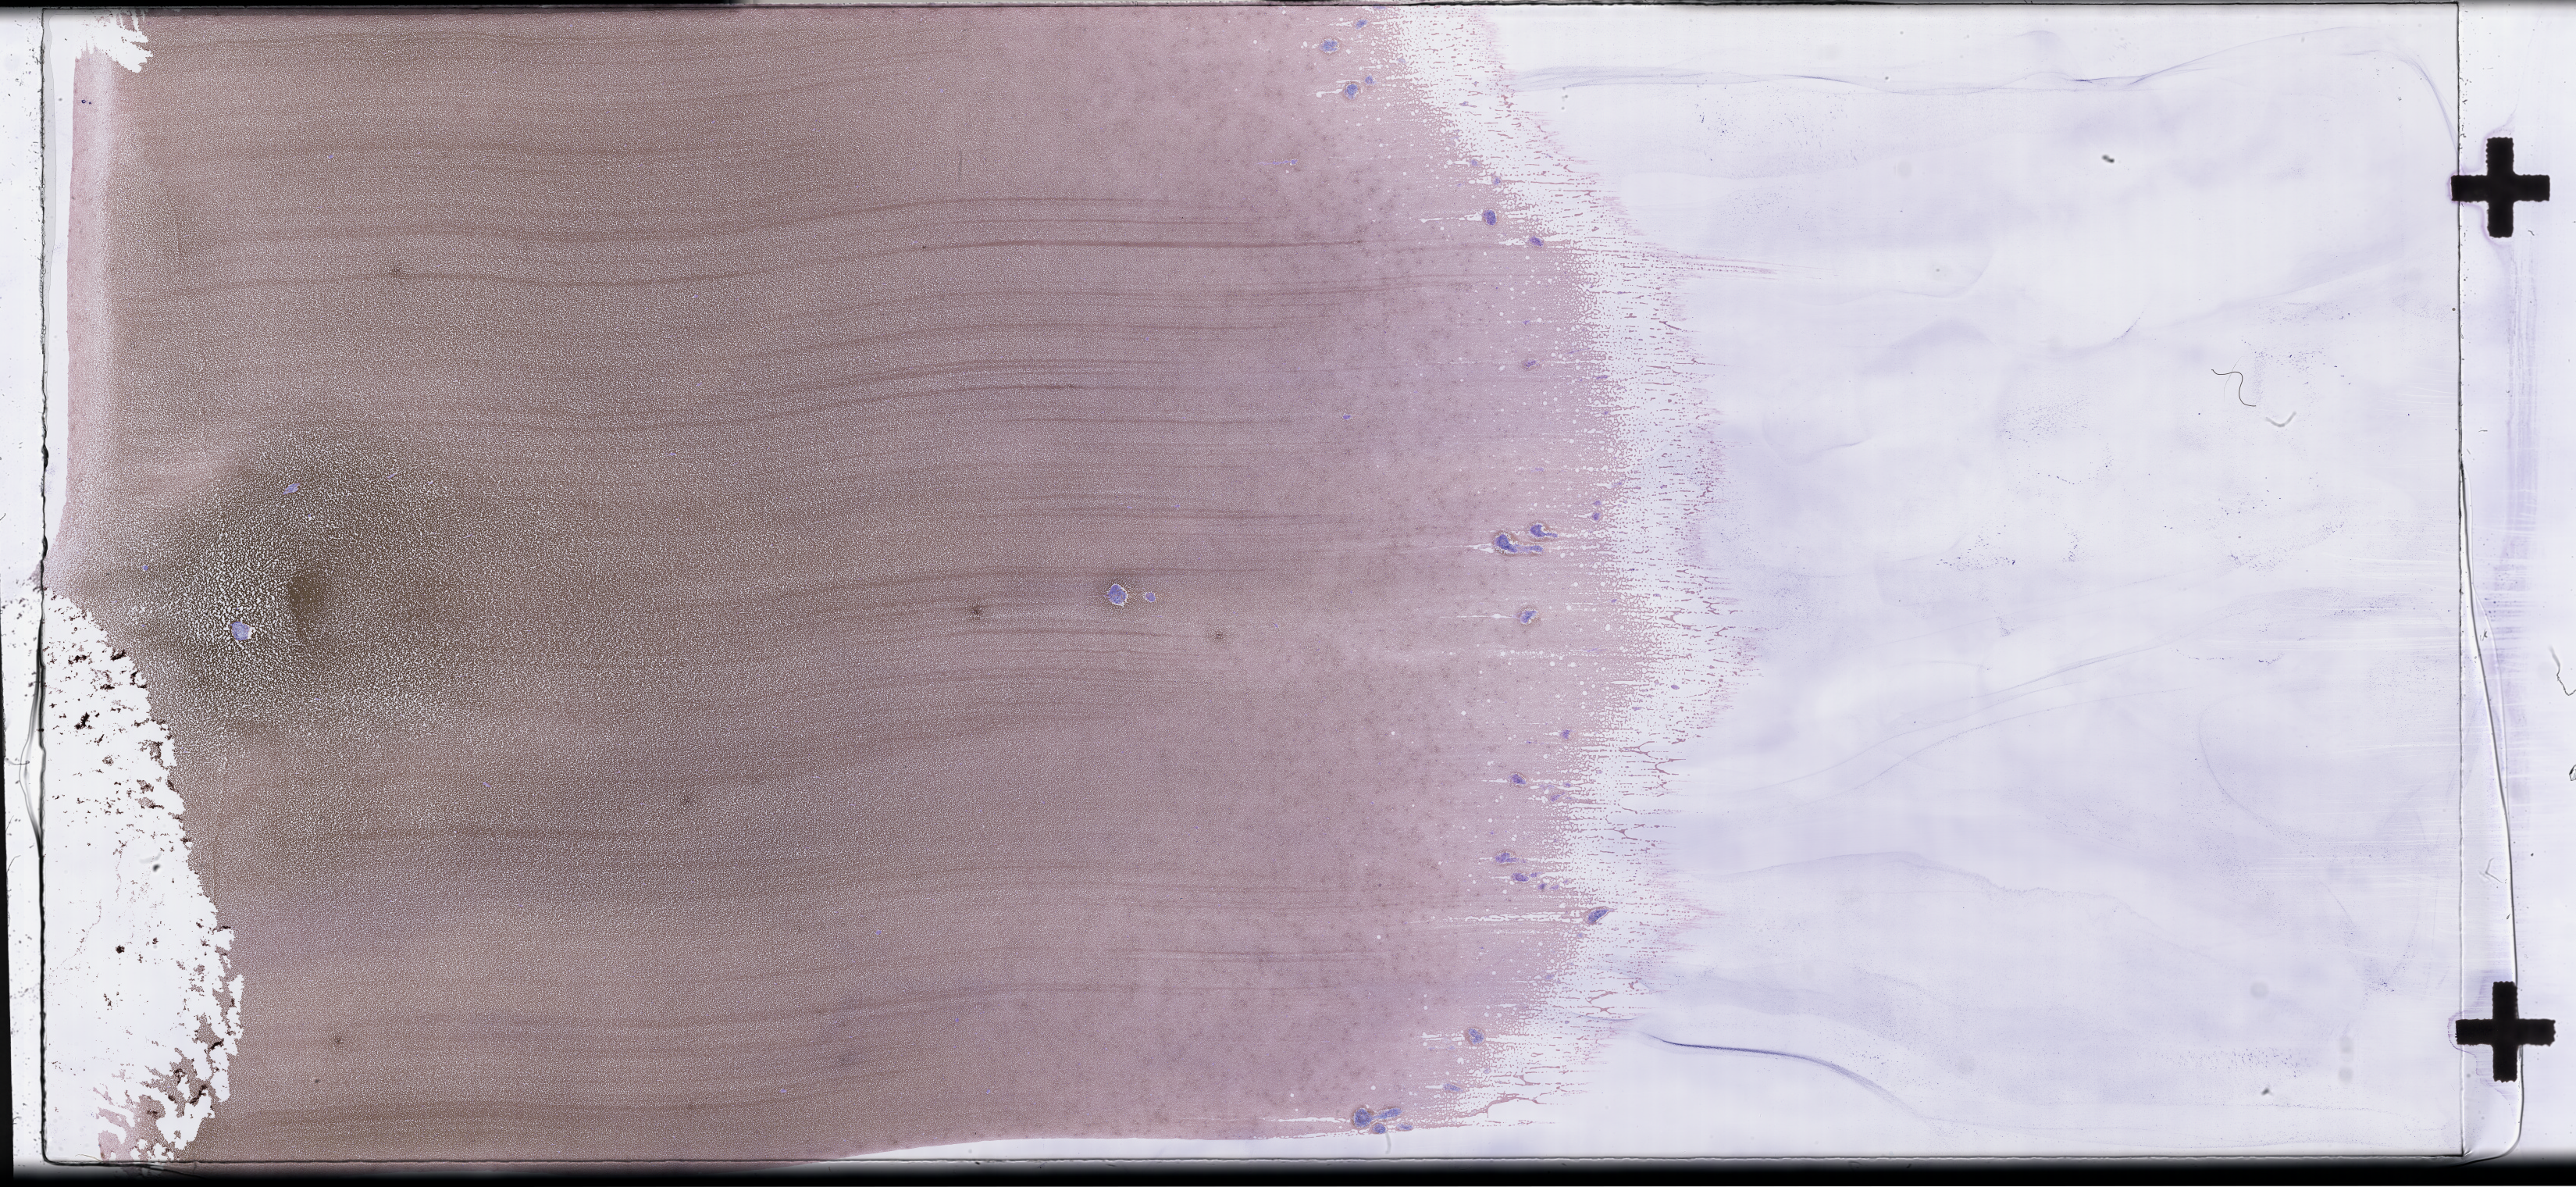
Whole-slide image of a whole blood smear, Wright–Giemsa stain, shown as a low-resolution overview of the whole scanned area (about 53.3 x 24.5 mm), collected on treatment. Patient sex: male.
Patient diagnosis: Plasma Cell Myeloma.